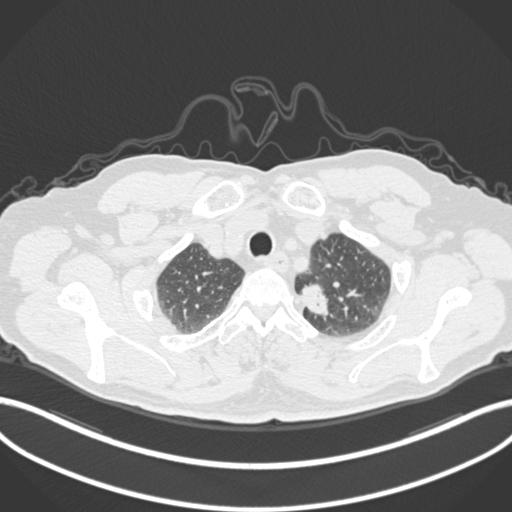
Chest CT, one axial slice. Slice 281 of 306 in the series (ordered by position). Reconstruction kernel B30f. Lung window (W 1500 / L -600 HU). 1 mm slice thickness. 512 × 512 image matrix, field of view 400 × 400 mm. Male patient, age 64 years. Case-level facts recorded for this patient, not image findings: clinical TNM (as recorded): T1c N0 M0.
Annotated regions visible in this slice (rectangle marked by the reading radiologist):
- lung tumour (recorded histology: adenocarcinoma): bounding box [x1, y1, x2, y2] px = [297, 280, 335, 325]